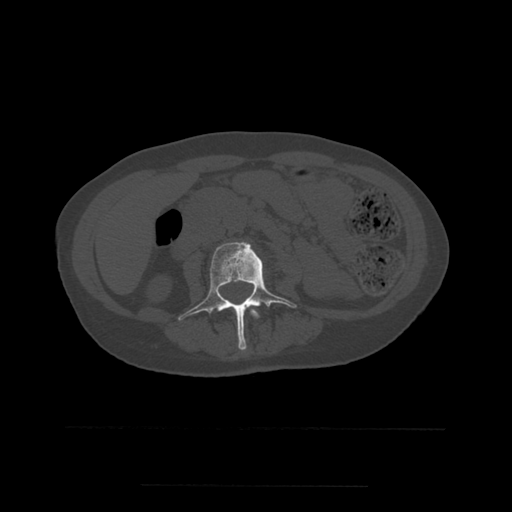
CT including the spine, one axial slice. Slice 191 of 544 in the series (ordered by position). Bone window (W 1800 / L 400 HU). 512 × 512 image matrix, field of view 350 × 350 mm. Patient age 58 years. Case-level facts recorded for this patient, not image findings: primary cancer: lung.
Structures marked on this image (semi-automatically segmented with operator editing):
- L2 vertebra: bounding box (x1, y1, x2, y2) in pixels: (251, 309, 260, 319)
- L3 vertebra: (178, 242, 297, 350)